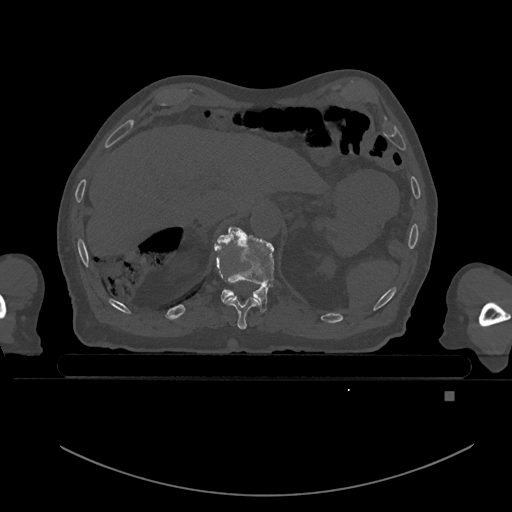
CT including the spine, one axial slice. Slice 57 of 969 in the series (ordered by position). Bone window (W 1800 / L 400 HU). 512 × 512 image matrix, field of view 456 × 456 mm. Male patient, age 82 years. Case-level facts recorded for this patient, not image findings: primary cancer: prostate; vertebrae with lytic lesions (as recorded): T11, T9, T8, T2.
Structures marked on this image (semi-automatic segmentation, software-assisted and operator-edited):
- T10 vertebra: bounding box <225,295,260,330> (left, top, right, bottom; pixels)
- T11 vertebra: <217,226,275,312>